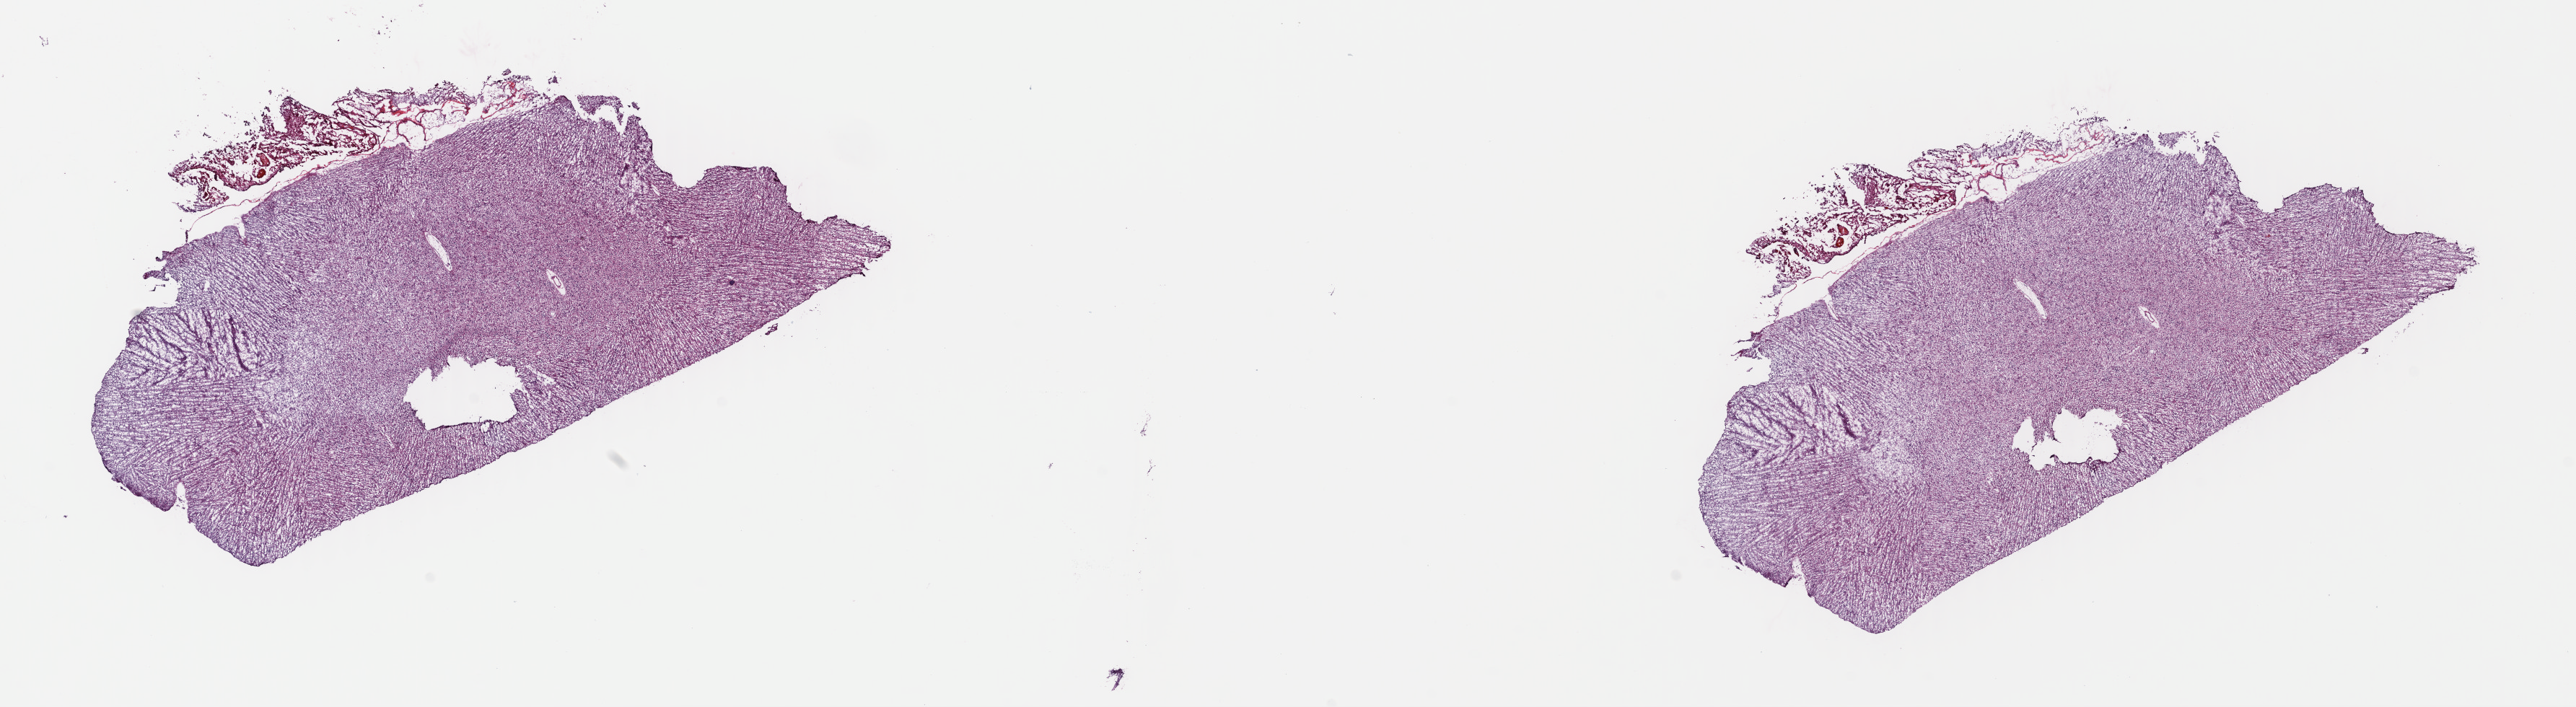
H&E-stained whole-slide image — low-resolution overview of the scanned area, about 28.1 x 7.7 mm (acquisition: 40x scan). Frozen section from the top of the tissue portion. Primary tumour sample from the brain. Patient: female, age at initial diagnosis 48 years. Histologic grade: G2 (moderately differentiated). Composition of this section per pathologist review: tumour cells 50%, tumour nuclei 90%, normal cells 10%, stromal cells 40%, necrosis 0%. Infiltration values recorded for this section: lymphocyte infiltration 0%, monocyte infiltration 0%, neutrophil infiltration 0%.
- histologic diagnosis: Oligodendroglioma, NOS (cerebrum)